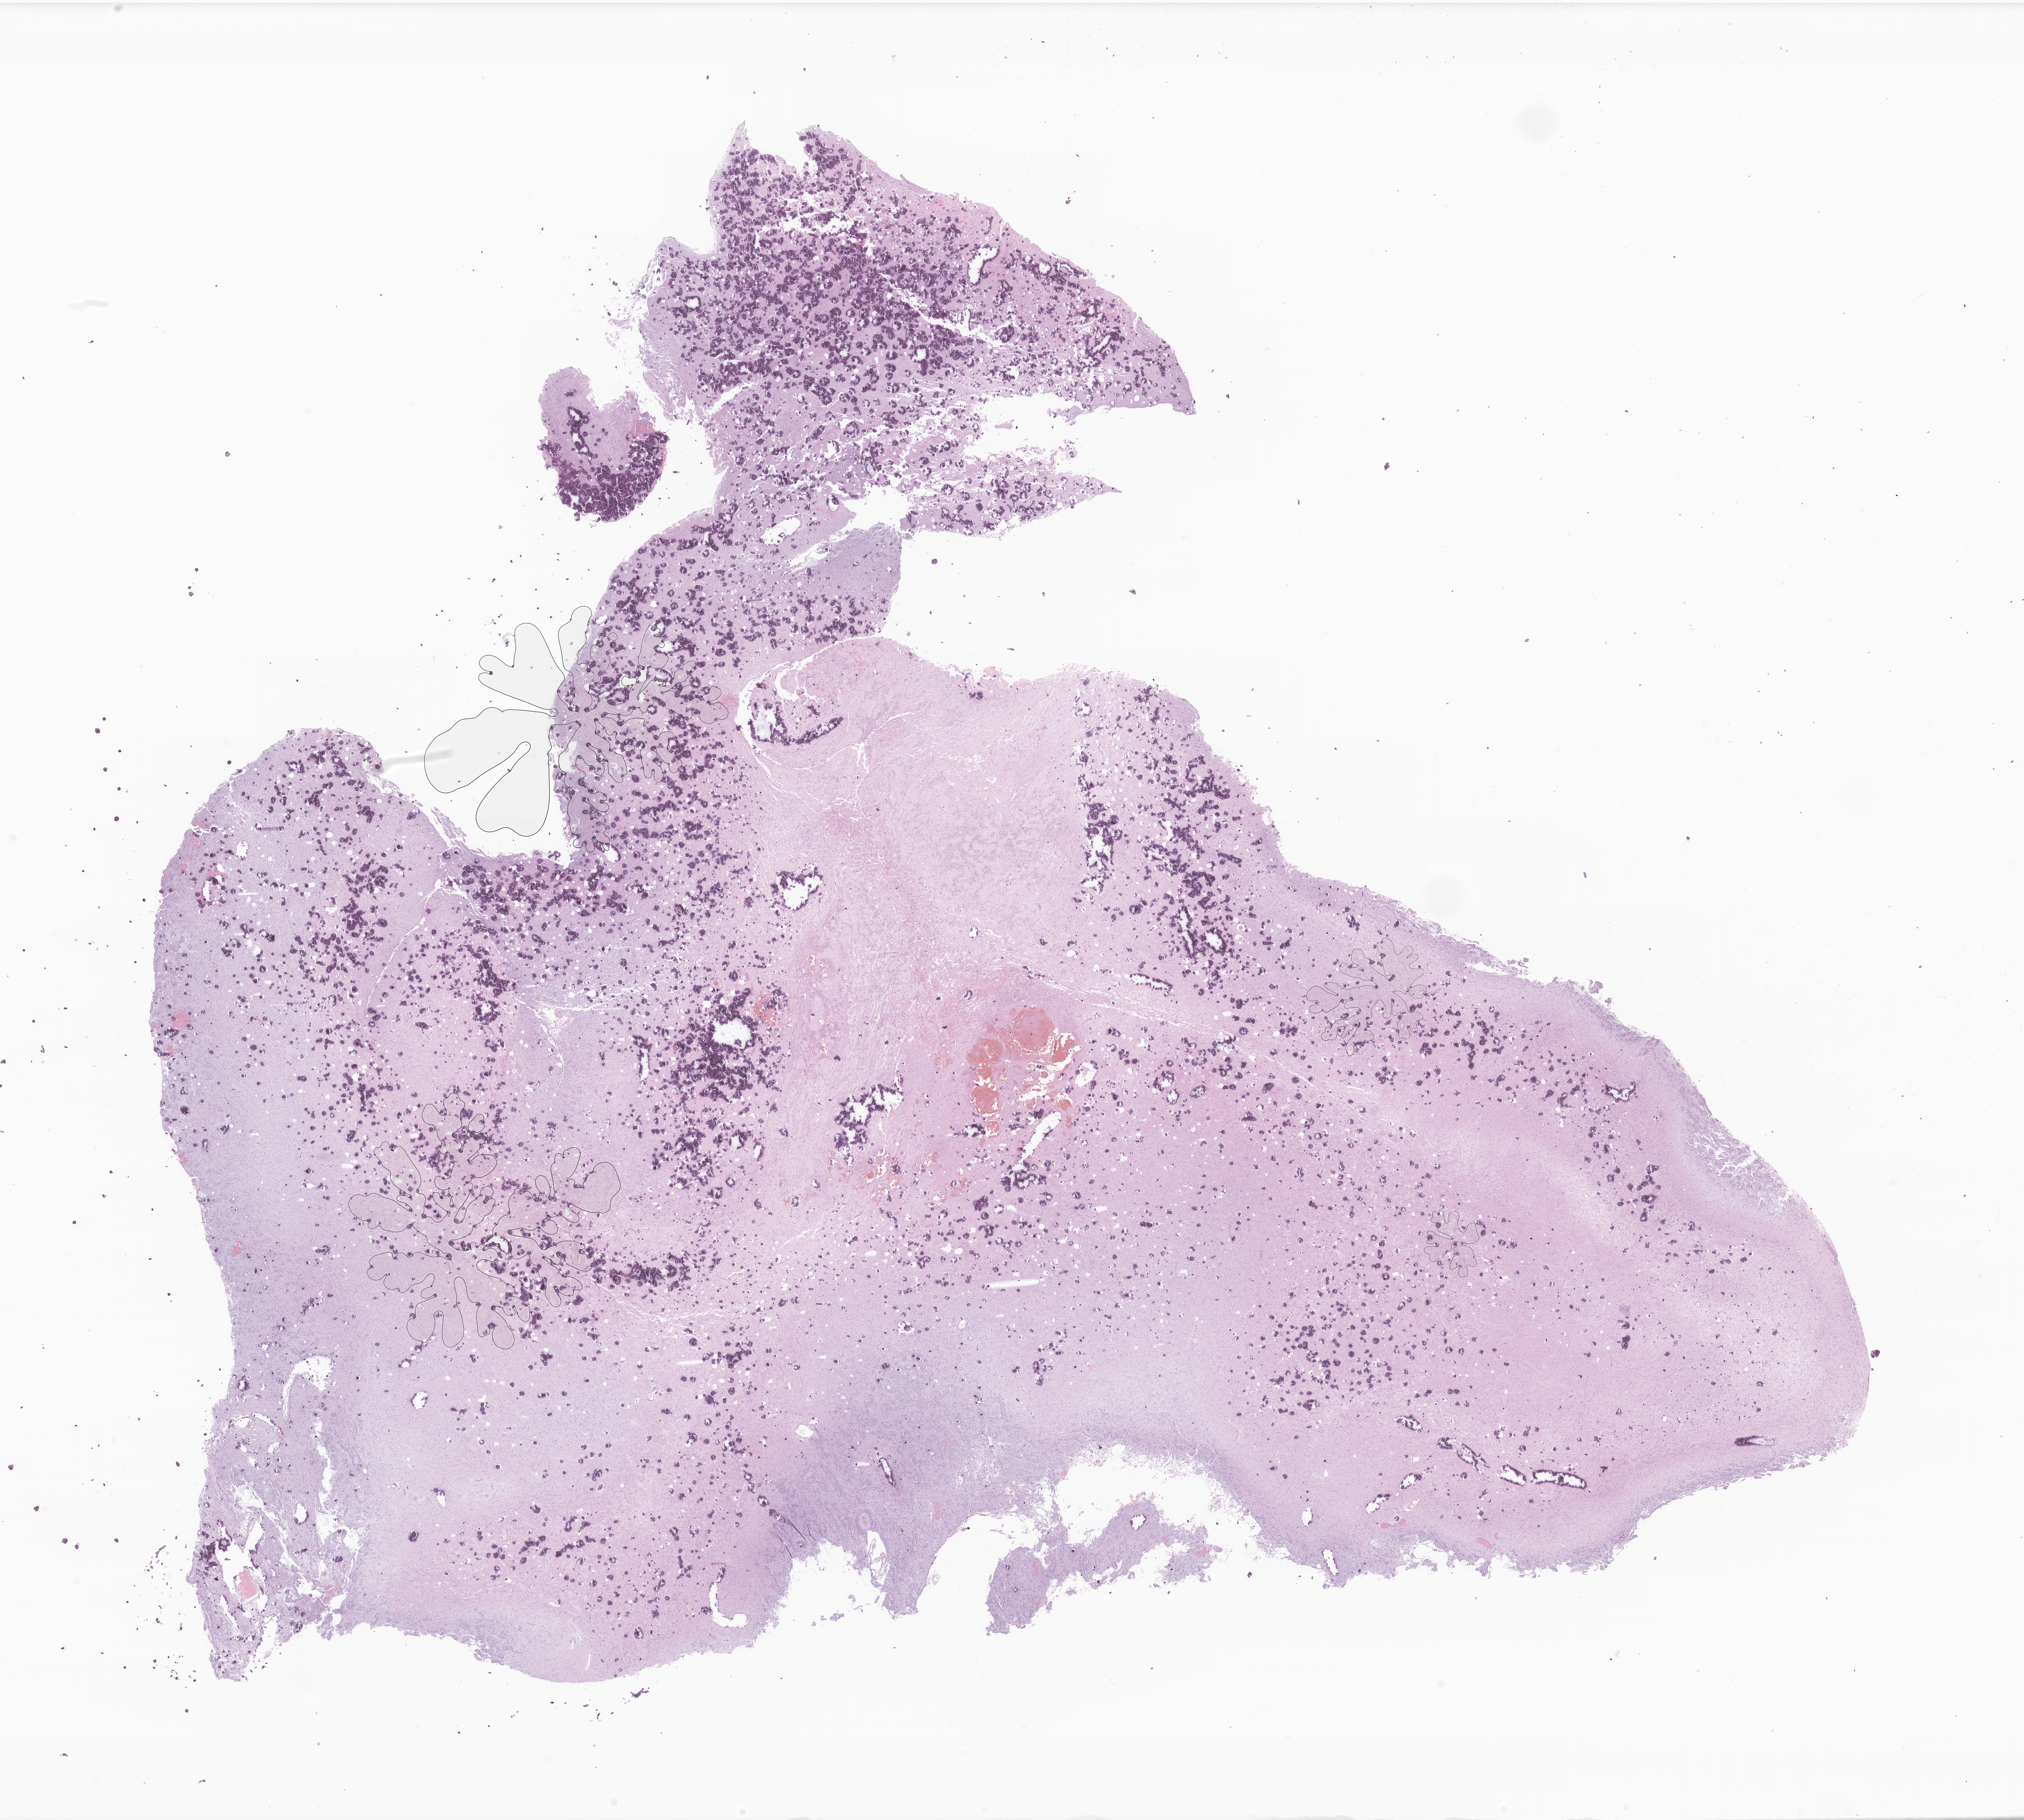
Digitized hematoxylin and eosin (H&E)-stained section of tumor tissue from the brain — shown as a low-resolution overview of the whole scanned area (about 25.8 x 23.2 mm), formalin-fixed paraffin-embedded section. Female patient, age 129 months (10 years 9 months).
* diagnosis (ICD-O-3 morphology term): Glioma, malignant